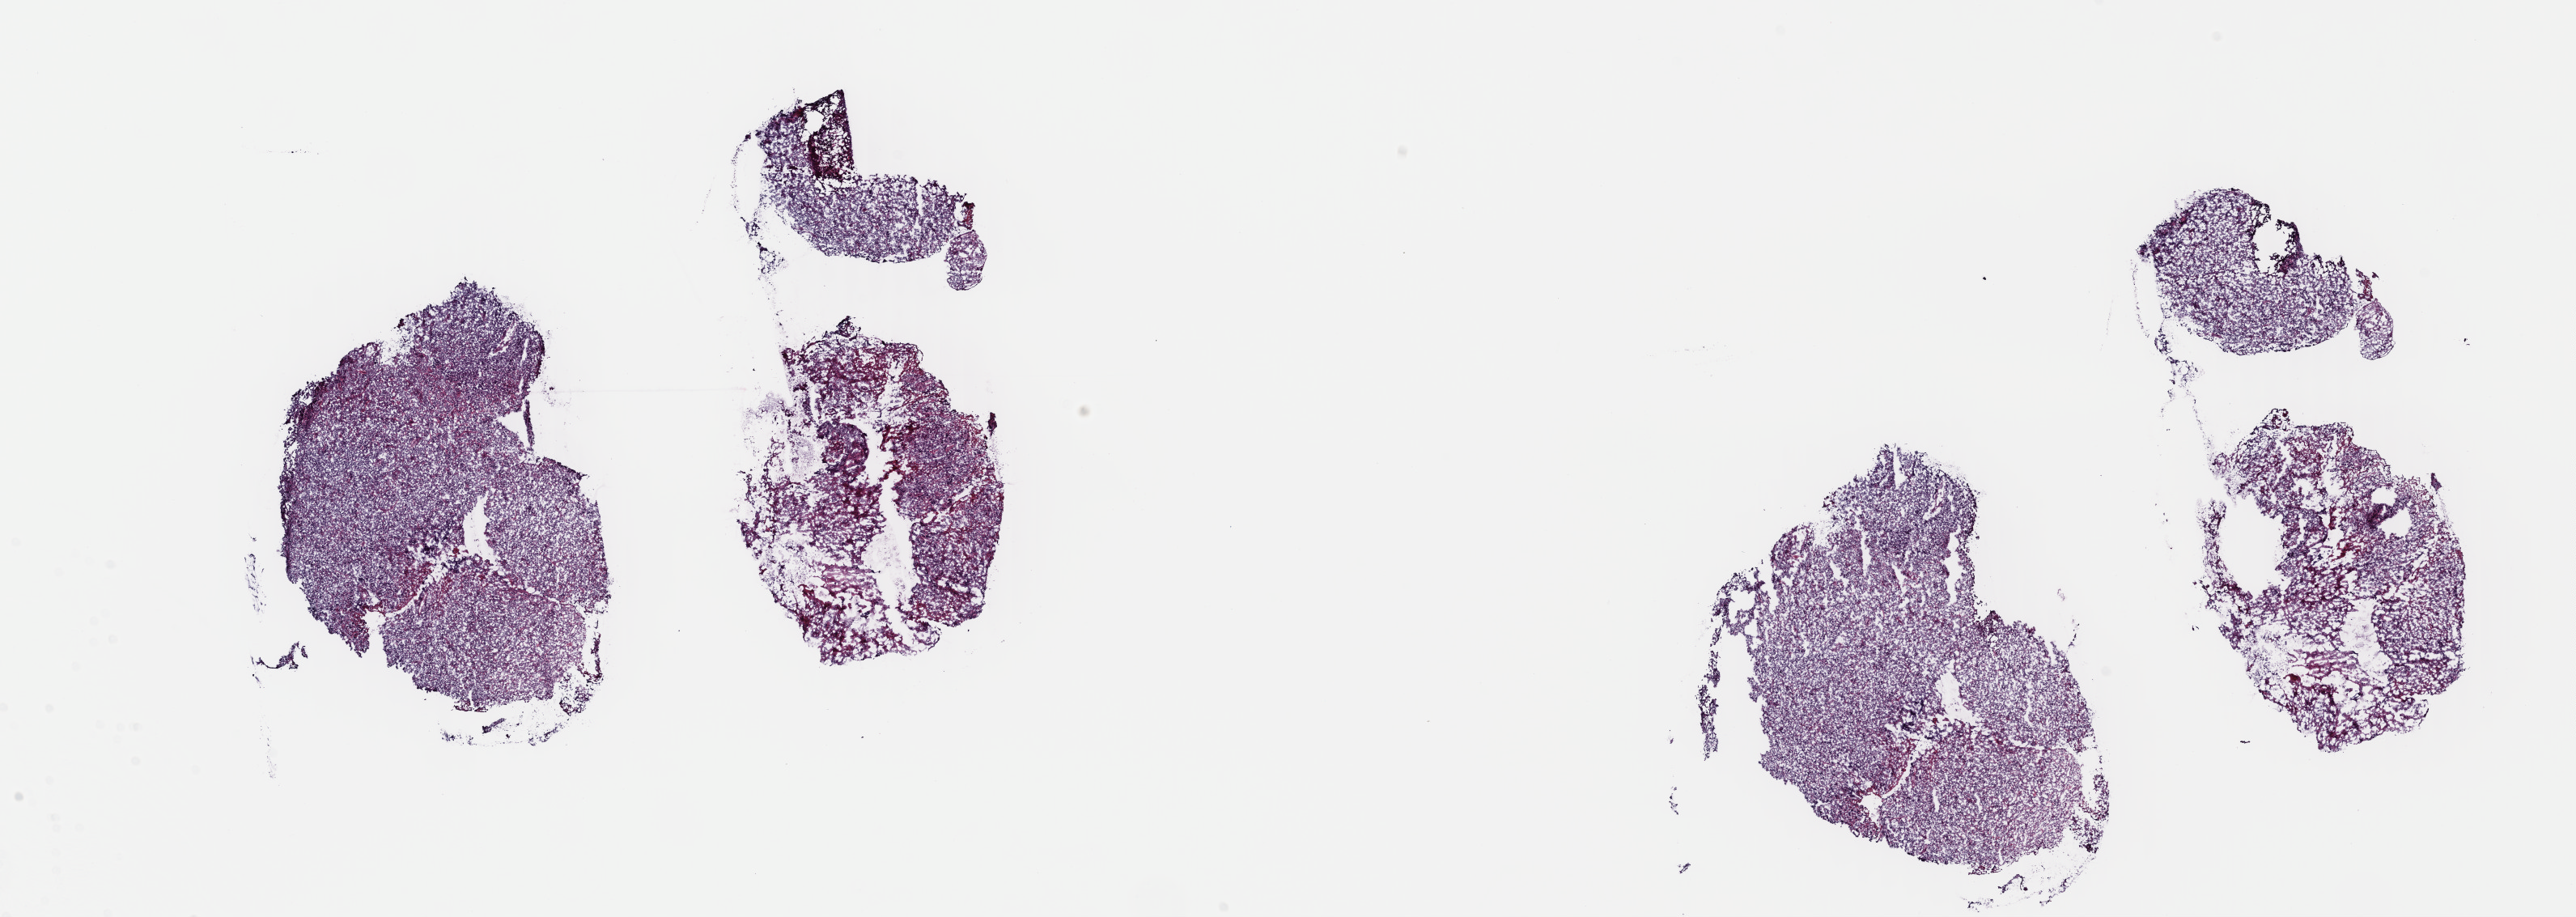
H&E-stained whole-slide image — whole scanned area (about 25.0 x 8.9 mm) shown as a low-resolution overview. Frozen section. Sample: primary tumour, lymphoid tissue. Male patient; age at initial diagnosis 63 years. Slide review estimates, as recorded: tumour cells 60%, tumour nuclei 70%, normal cells 10%, stromal cells 30%, necrosis 0%. Infiltration values recorded for this section: lymphocyte infiltration 70%, monocyte infiltration 10%, neutrophil infiltration 0%.
Pathologic diagnosis: Primary diffuse large B-cell lymphoma of the CNS (brain stem).